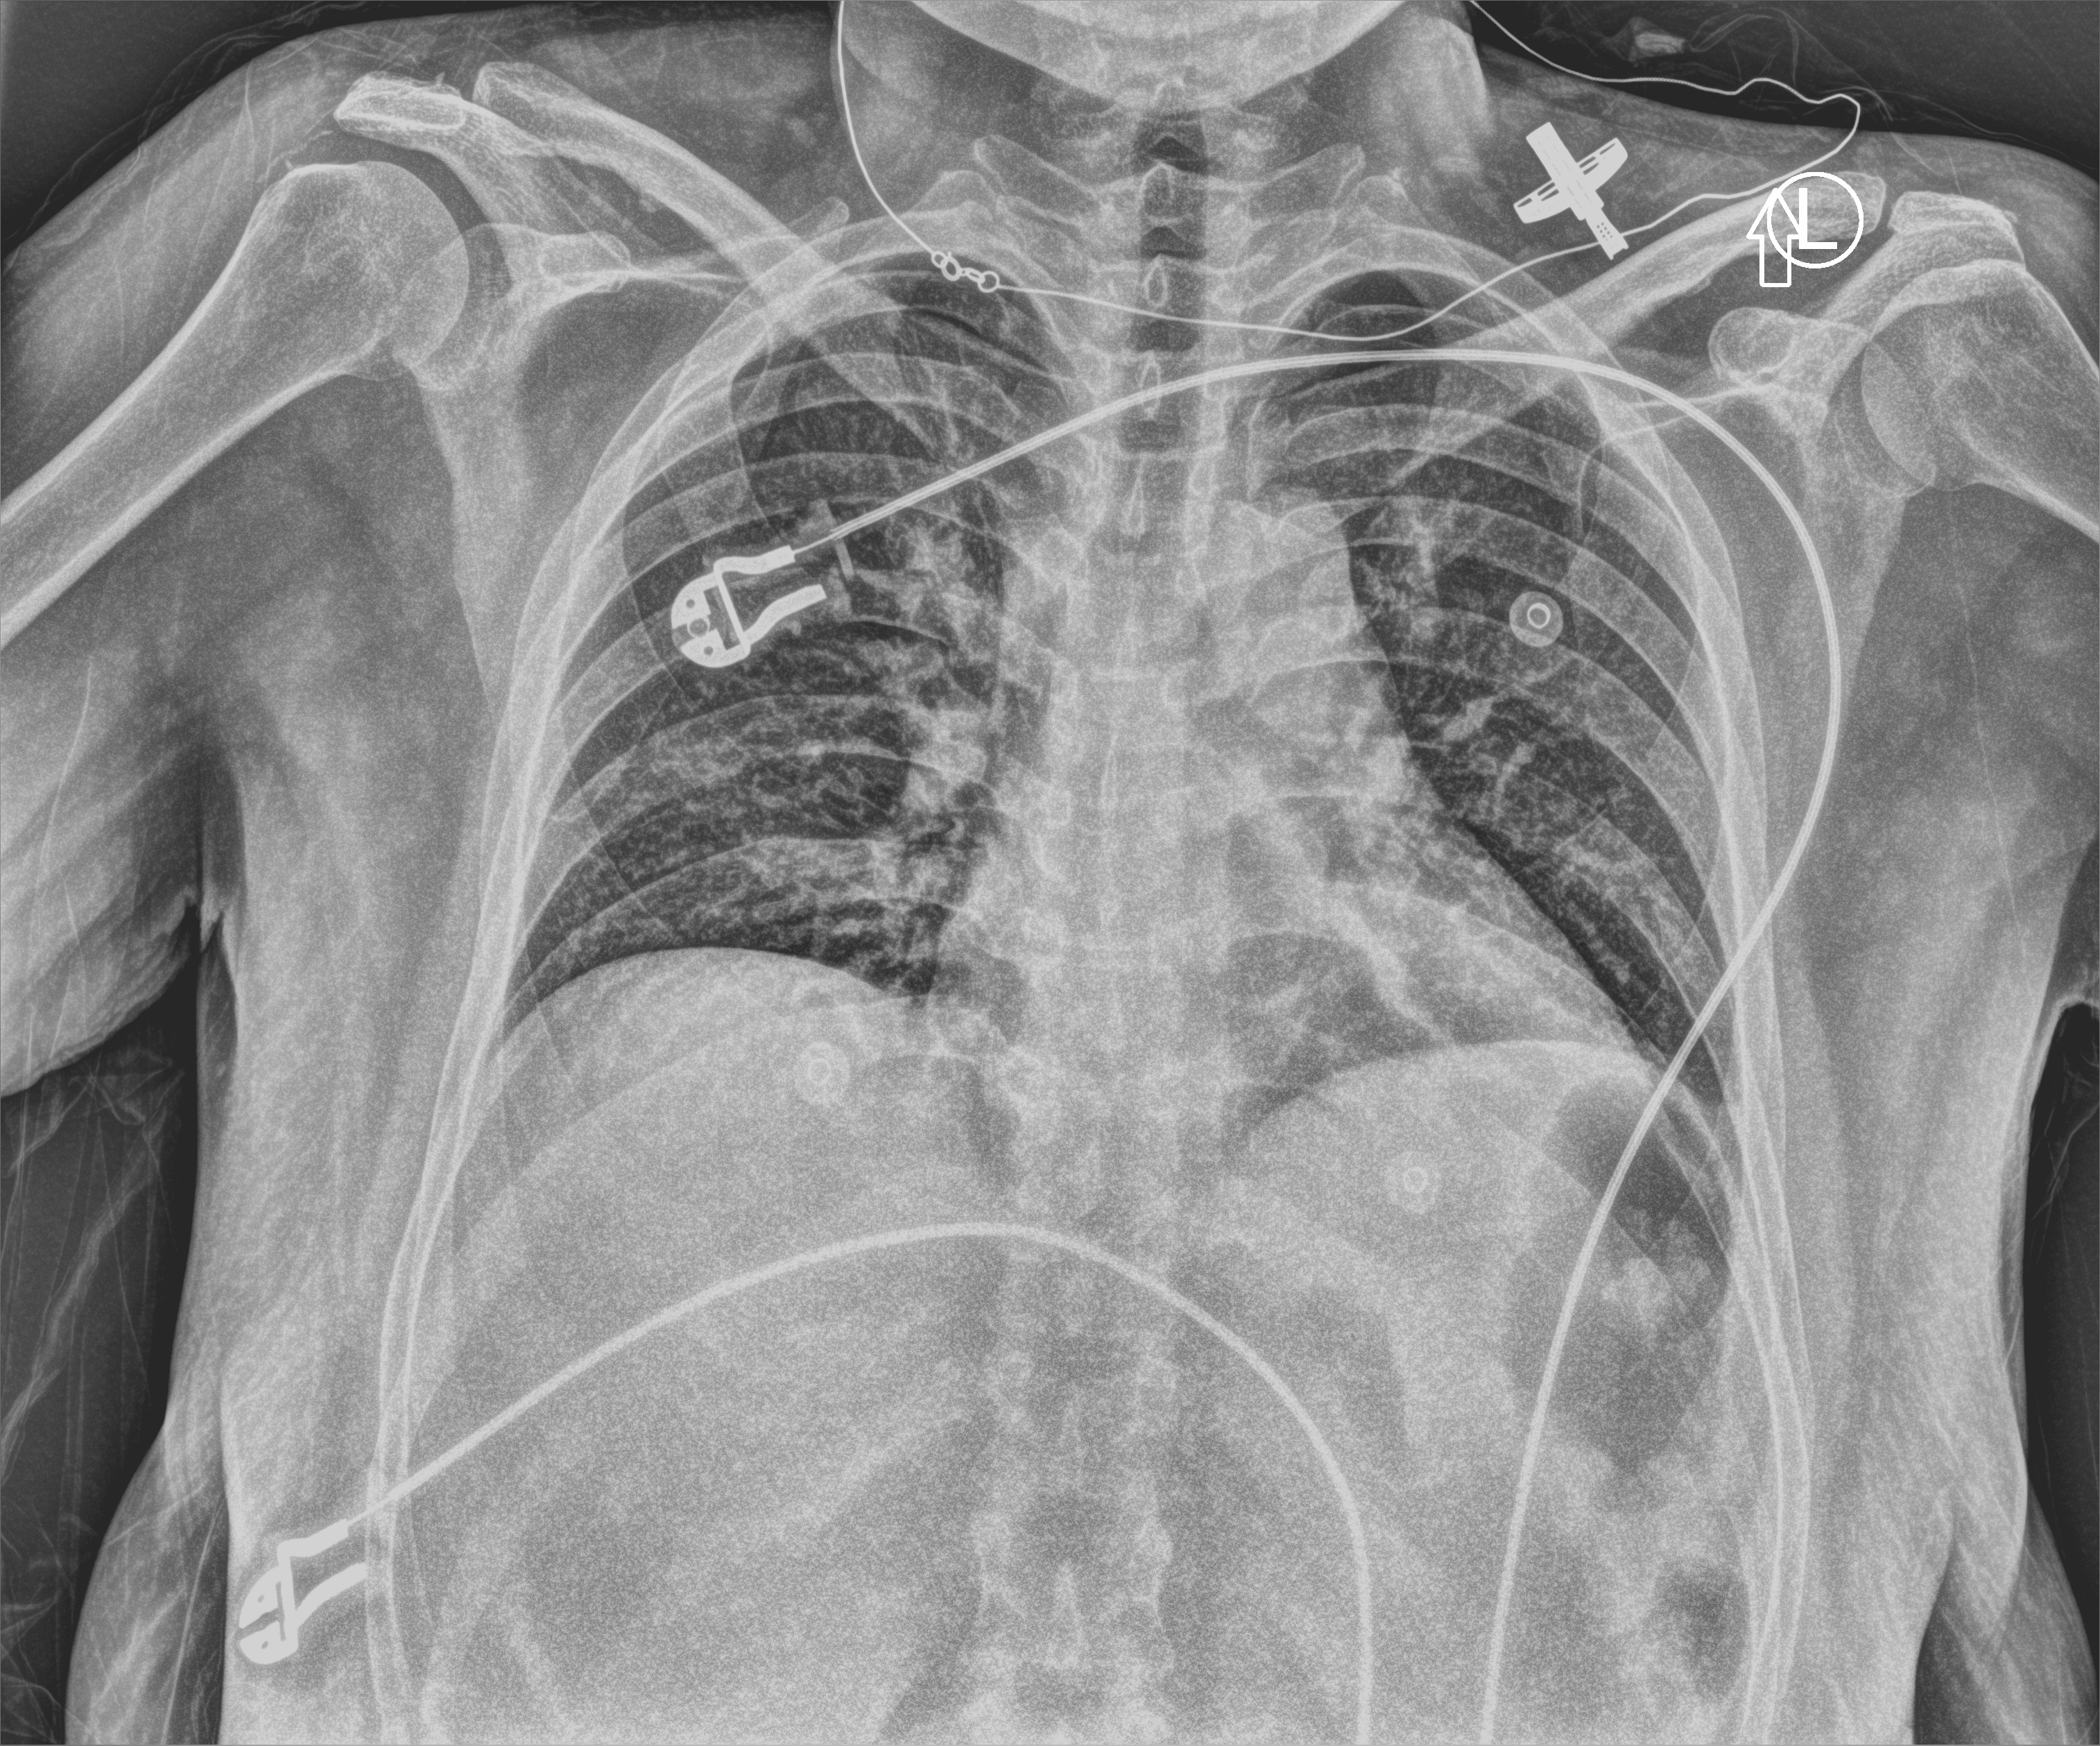
Chest X-ray (portable), anteroposterior (AP) projection. Female patient hospitalised with COVID-19, age 18–59 years.
Hospital-stay facts (about this admission, not read from this image; timing relative to this image not recorded): admitted to intensive care during this hospital stay: no; mechanically ventilated during this hospital stay: no.